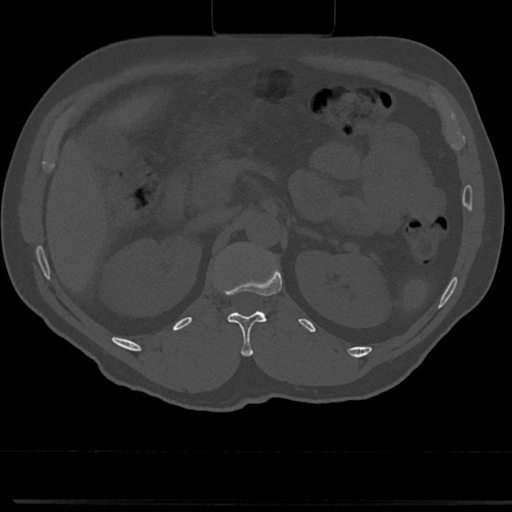
CT including the spine, one axial slice; slice 124 of 817 in the series (ordered by position); reconstruction kernel Br40s/3; 120 kVp; bone window (W 1800 / L 400 HU); 0.5 mm slice thickness; 512 × 512 image matrix, field of view 355 × 355 mm. Patient: male, 61 years. From the clinical record (not read from this slice): primary cancer: prostate.
Outlined on this slice (semi-automatic segmentation, software-assisted and operator-edited):
- L1 vertebra: bounding box [x1, y1, x2, y2] px = [212, 241, 274, 320]
- T12 vertebra: [225, 311, 267, 356]